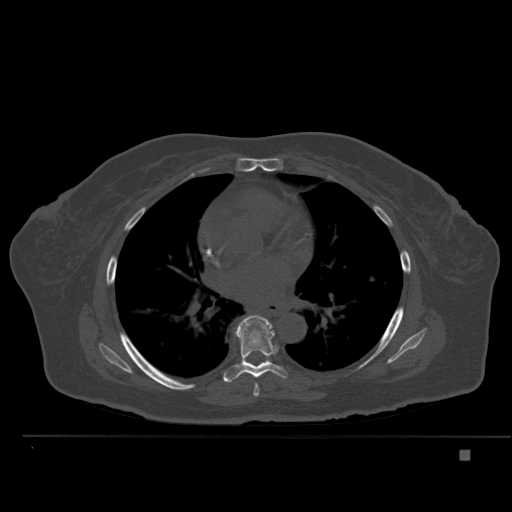
CT including the spine, one axial slice. Position 326 of 477 along the scan axis. Bone window (W 1800 / L 400 HU). 1.5 mm slice thickness. 512 × 512 image matrix, field of view 422 × 422 mm. Female patient, age 74 years. From the clinical record (not read from this slice): primary cancer: colon.
Structures marked on this image (semi-automatically segmented with operator editing):
- T6 vertebra: bounding box [x1, y1, x2, y2] px = [253, 384, 259, 397]
- T7 vertebra: [223, 315, 287, 383]
- T8 vertebra: [266, 360, 270, 362]